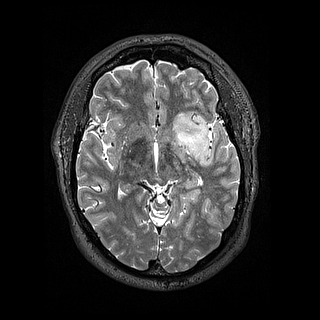
Brain MRI from a brain-tumour surgery series, one axial slice; slice 90 of 144 in the series (ordered by position); 1.2 mm slice thickness; 320 × 320 image matrix, field of view 254 × 254 mm. From the clinical record (not read from this slice): histopathology: Astrocytoma; WHO grade: 2; IDH mutation: yes.
Structures marked on this image (expert manual segmentation):
- tumour: box from (x=173, y=109) to (x=210, y=161) px